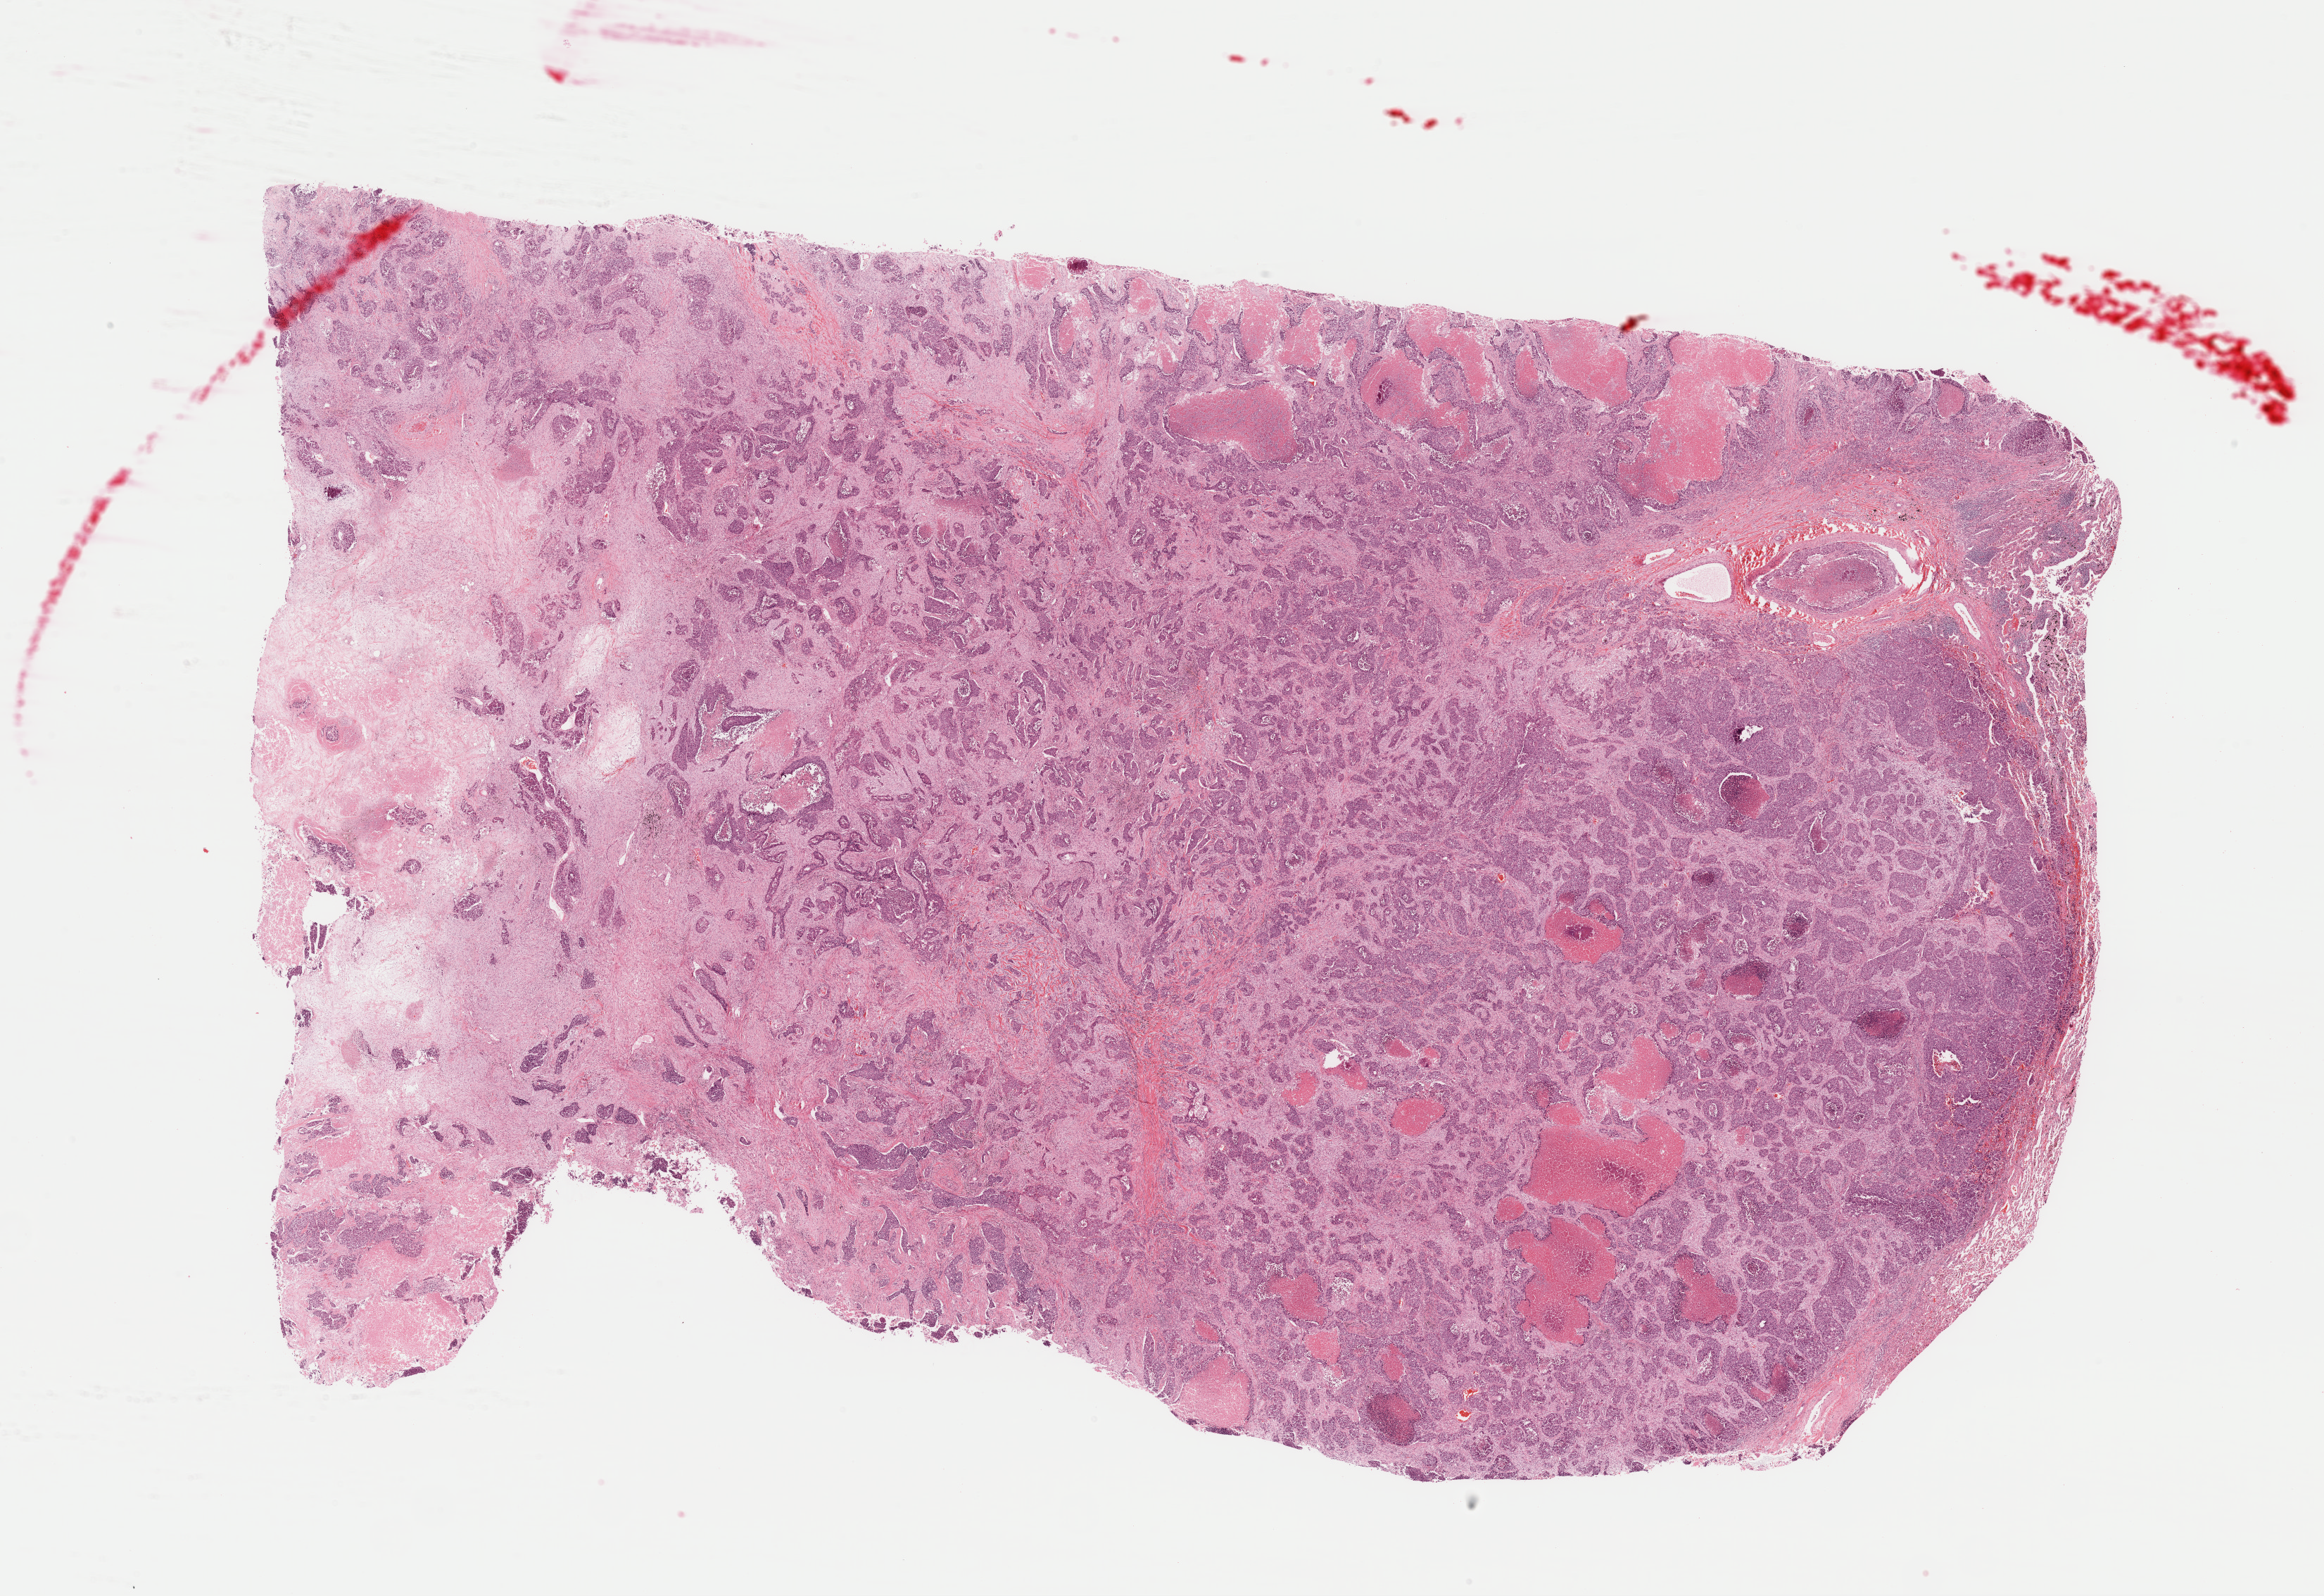
Whole-slide histology image, Hematoxylin and eosin (H&E) stained — a low-resolution overview of the entire scanned area, about 26.1 x 17.9 mm (from a 40x scan), formalin-fixed paraffin-embedded (FFPE) diagnostic section, primary tumour sample from the lung. Male, age 48 years at initial diagnosis.
Laterality: right. Diagnosis: Adenocarcinoma, NOS (upper lobe, lung). AJCC pathologic stage: IIA (7th edition).